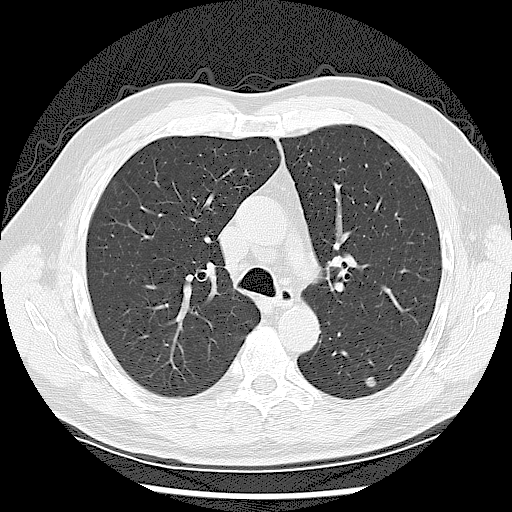
Low-dose screening chest CT, axial slice, baseline screening round, lung window (W 1500 / L -600 HU), 2.5 mm slice thickness, slice 43 of 123 in the series. Male, age 65 years at enrolment.
• Lesion marked by an expert reader, bounding box <350,365,400,404> (left, top, right, bottom; pixels).
• Screening reader's record for this exam (one nodule recorded; not confirmed to be the boxed lesion): non-calcified nodule or mass ≥4 mm, left lower lobe, 7 × 7 mm, smooth margins, soft tissue attenuation.
• Participant outcome: lung cancer diagnosed 375 days after this screen (after the second annual screen) — adenocarcinoma, NOS, left lower lobe, well differentiated (G1), stage IB (AJCC 6th edition), 10 mm at pathology.